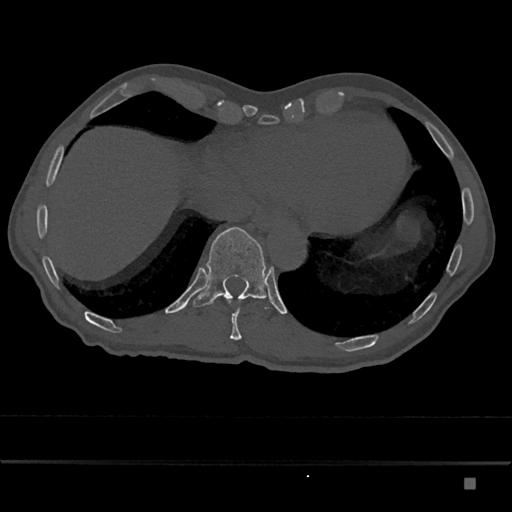
CT including the spine, one axial slice. Position 701 of 797 along the scan axis. Bone window (W 1800 / L 400 HU). 512 × 512 image matrix, field of view 390 × 390 mm. Patient: male, 72 years. From the clinical record (not read from this slice): primary cancer: prostate.
Outlined on this slice (semi-automatically segmented with operator editing):
- T10 vertebra: bounding box <227,298,242,340> (left, top, right, bottom; pixels)
- T11 vertebra: <193,227,269,310>